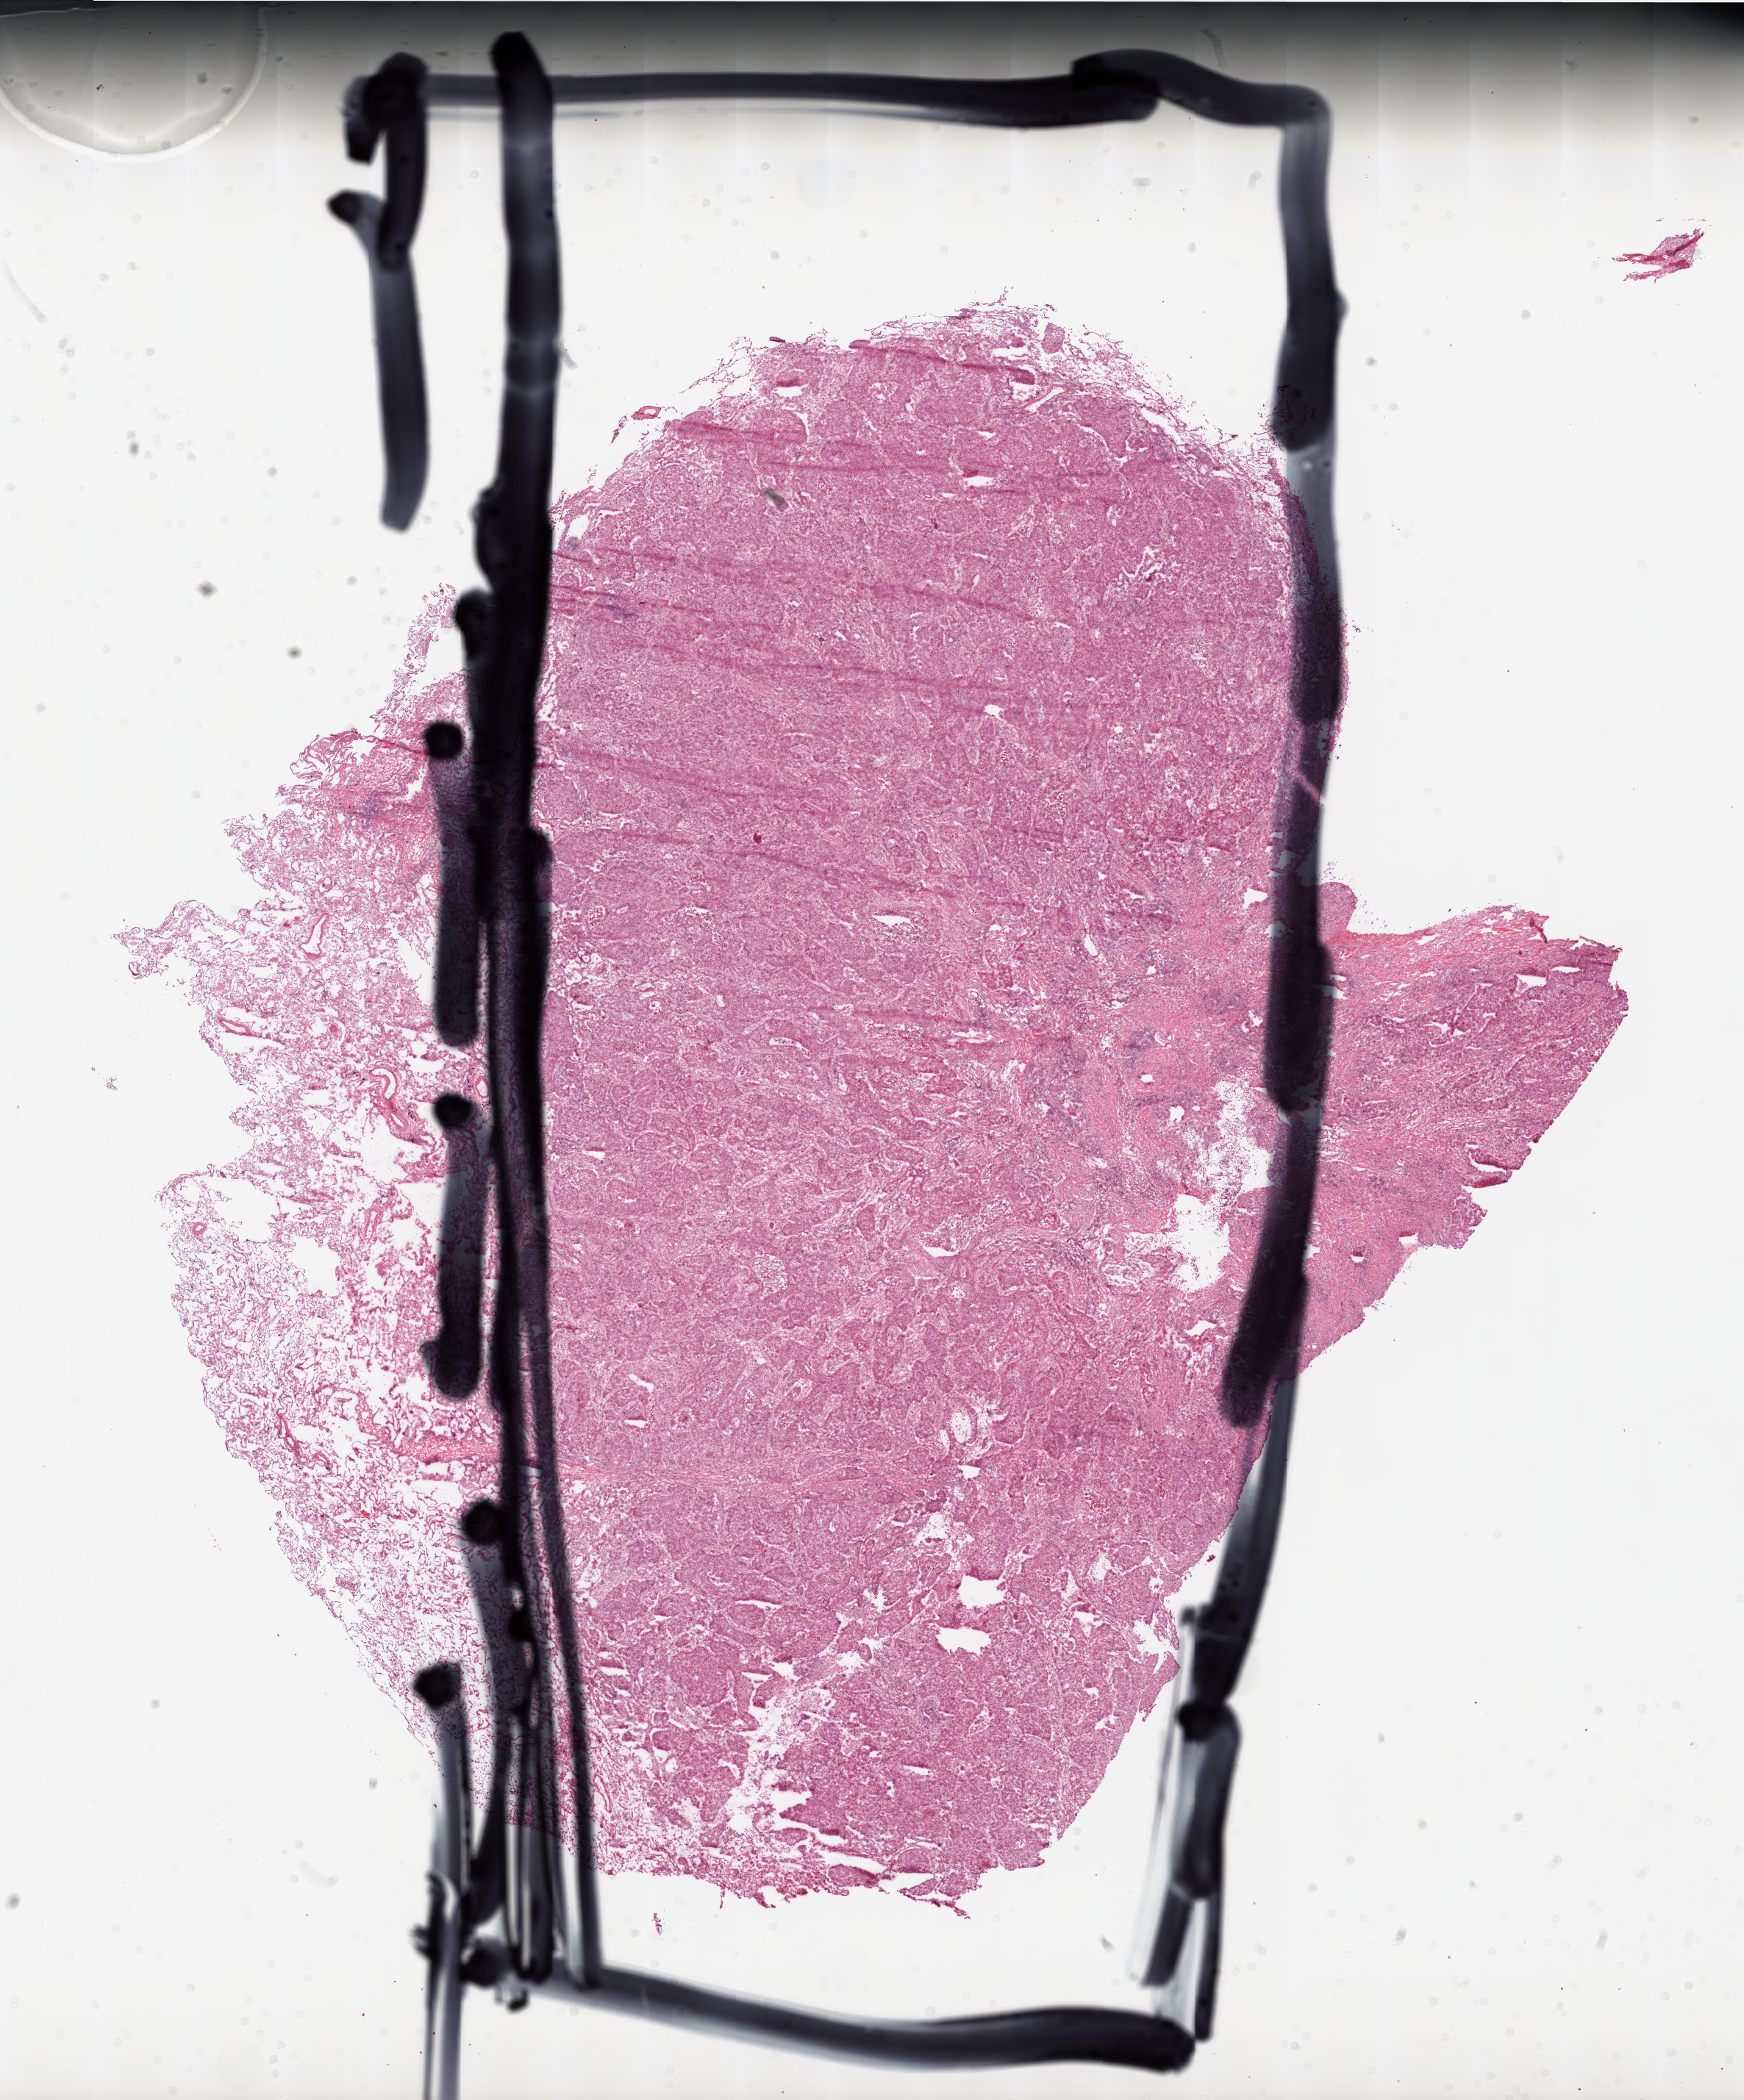
Digitized Hematoxylin and eosin (H&E) stained tissue section (whole slide) — shown as a low-resolution overview of the whole scanned area (about 19.0 x 22.9 mm, from a 20x scan), frozen section from the top of the tissue portion, sample: primary tumour, lung. Male, age 71 years at initial diagnosis. Pathologist review of this section (percent, as recorded): tumour nuclei 90%, necrosis 5%.
Histologic diagnosis: Squamous cell carcinoma, NOS.